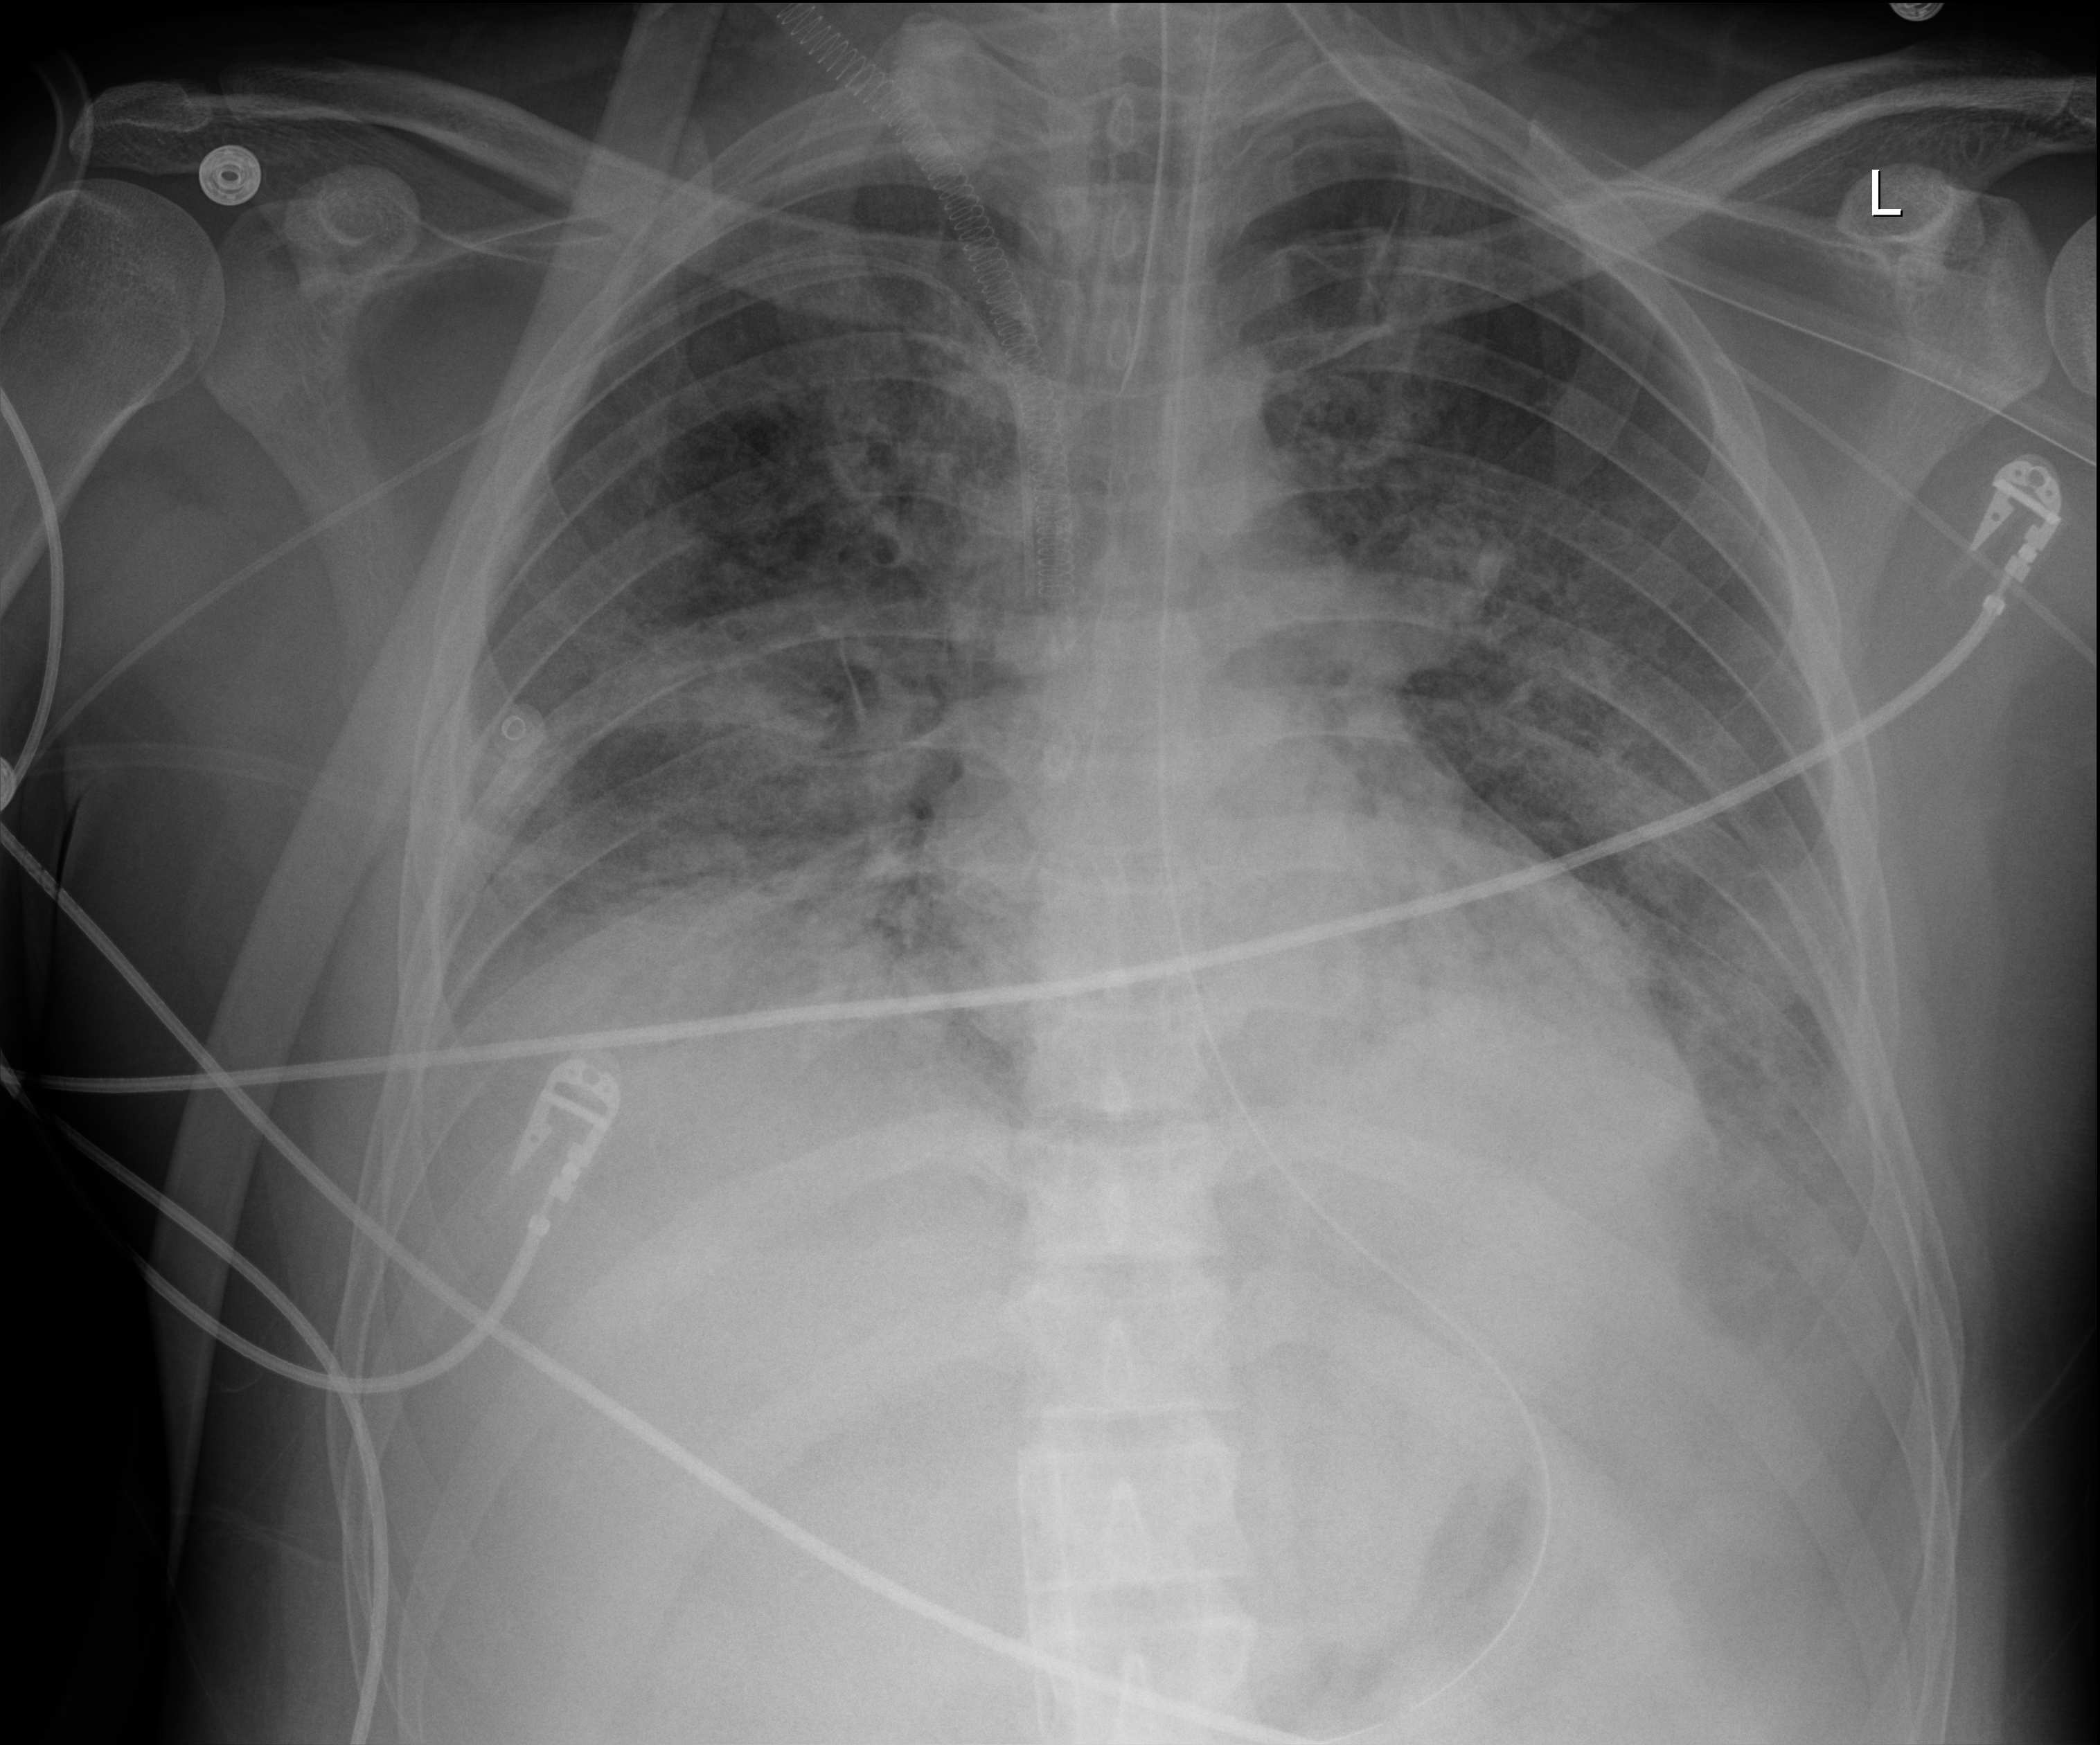
Chest X-ray. Adult patient hospitalised with COVID-19, age 18–59 years.
Hospital-stay facts (about this admission, not read from this image; timing relative to this image not recorded):
- length of hospital stay: 60 days
- admitted to intensive care during this hospital stay: yes